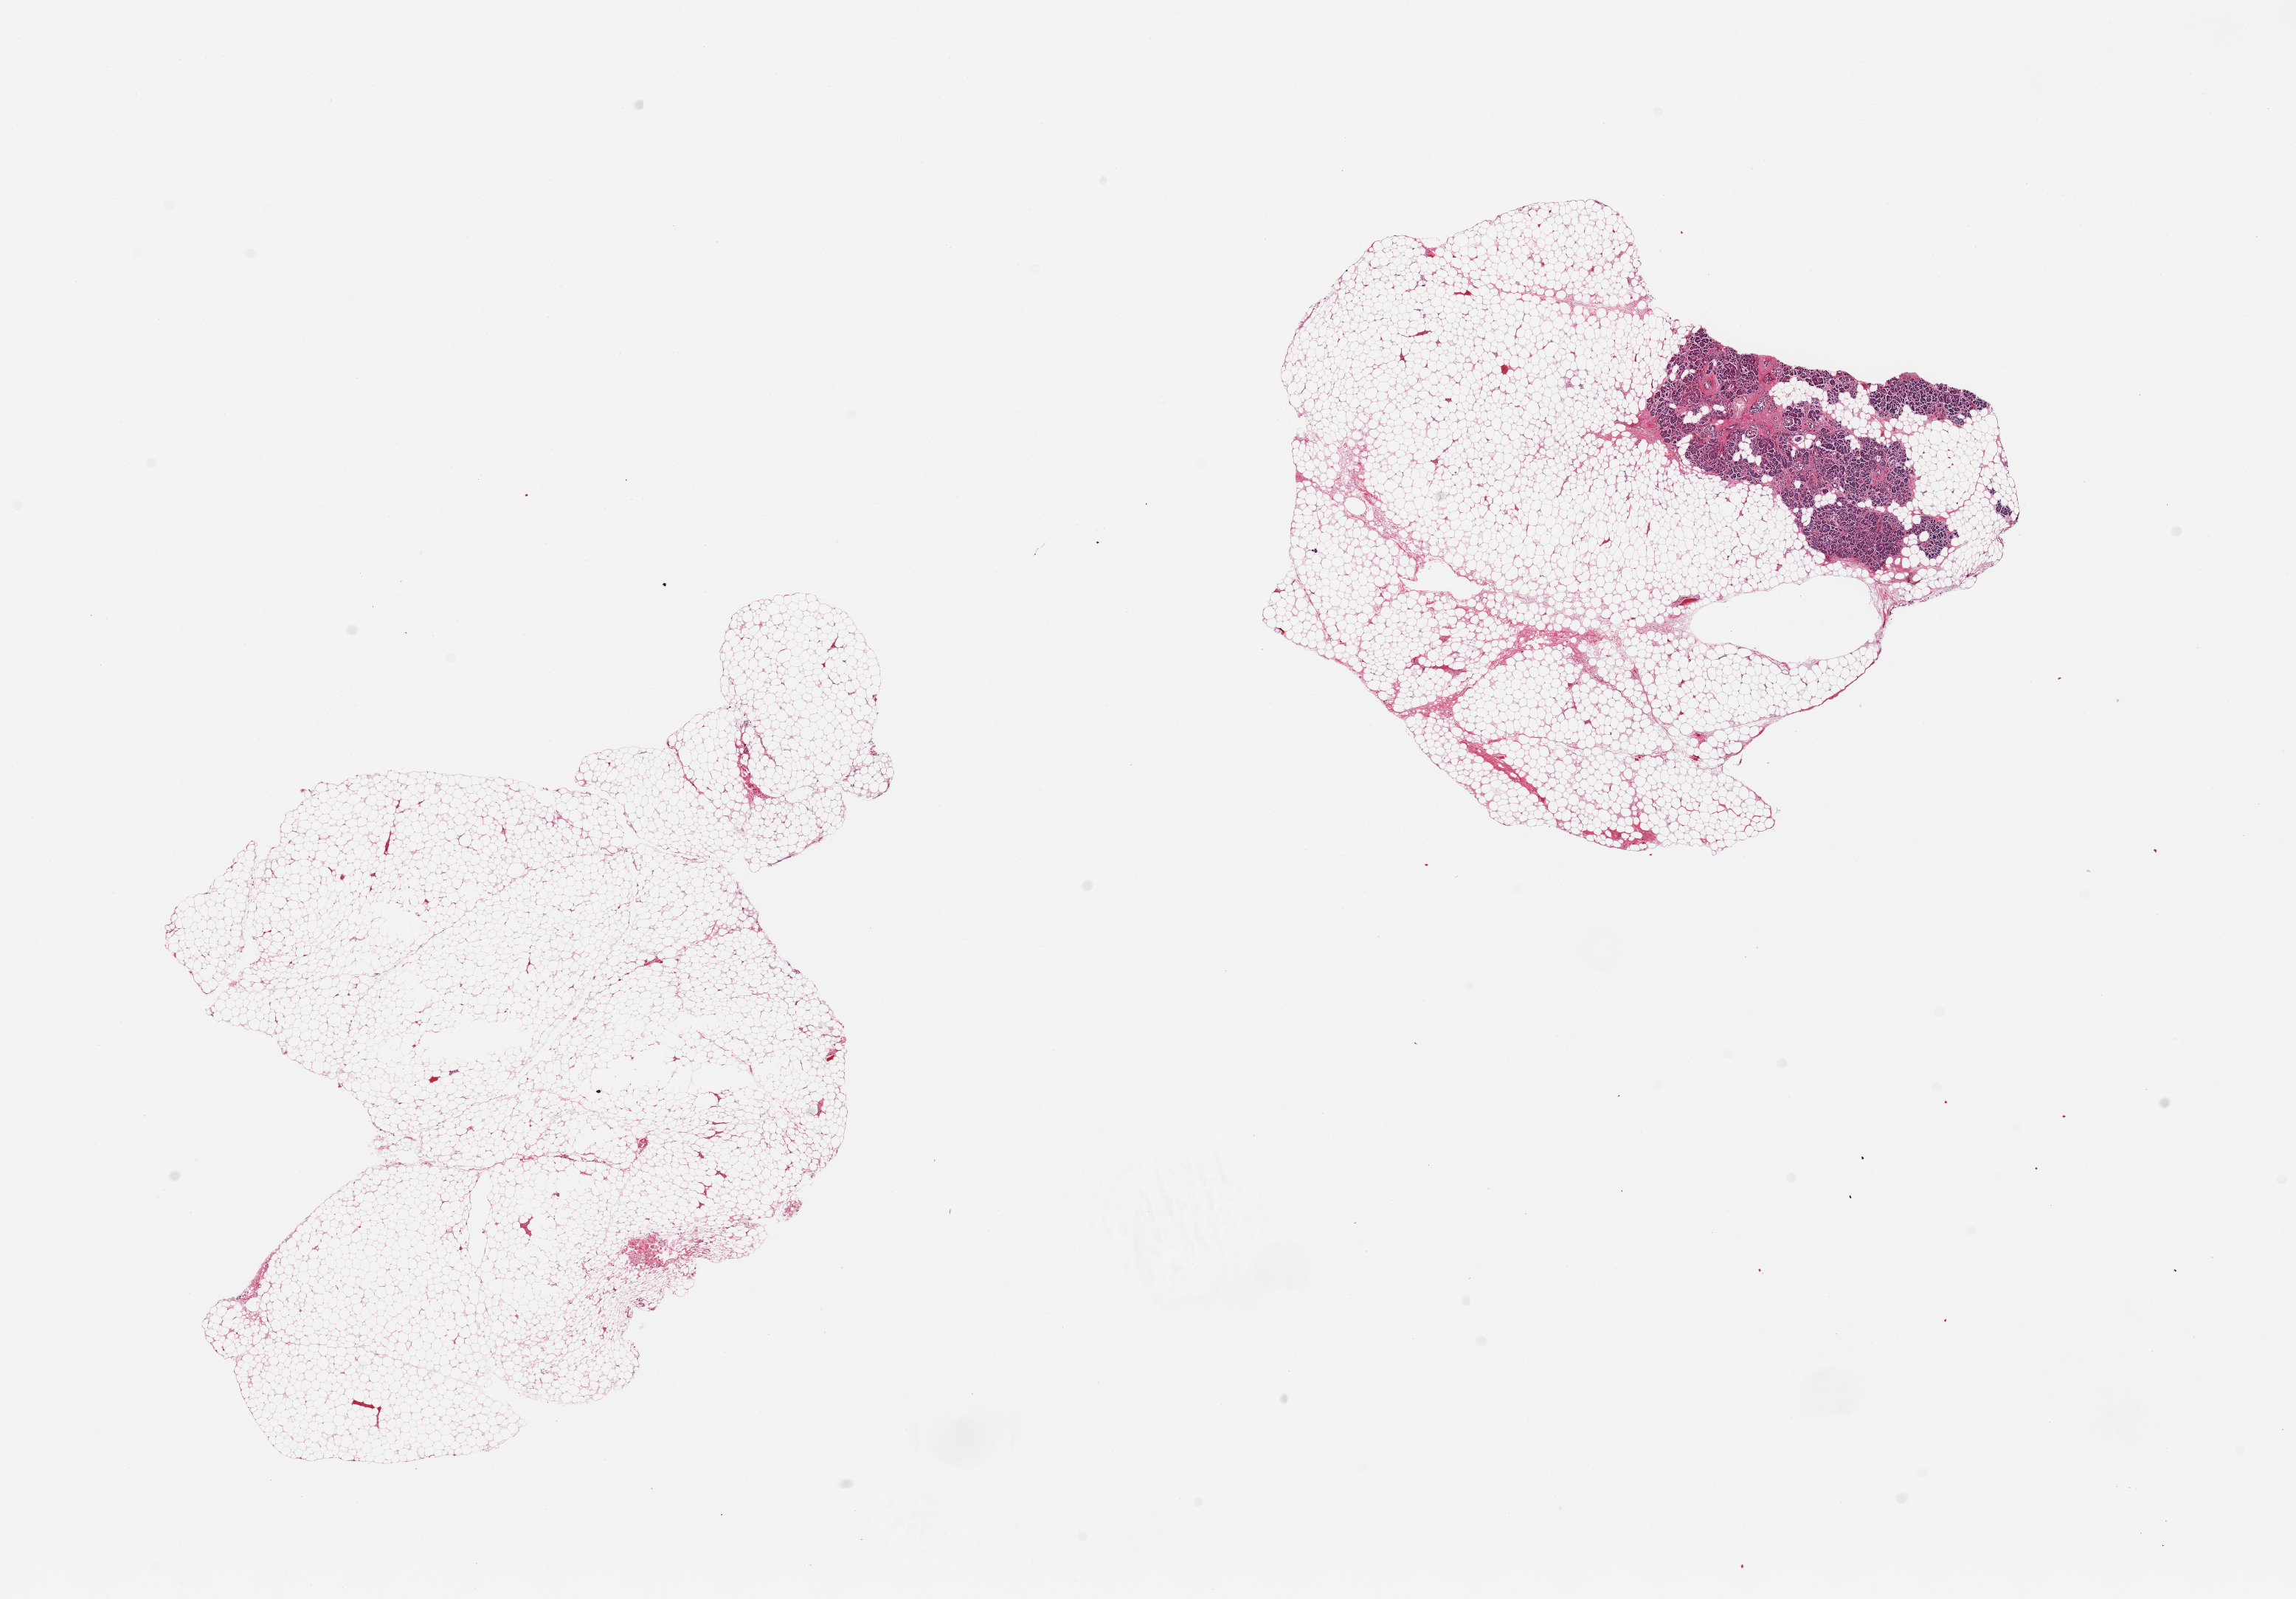
Whole-slide image, H&E stain — whole scanned area (about 24.6 x 17.1 mm) shown as a low-resolution overview.
Specimen: PAXgene-fixed, paraffin-embedded tissue; section of pancreas (target tissue); donor tissue sample.